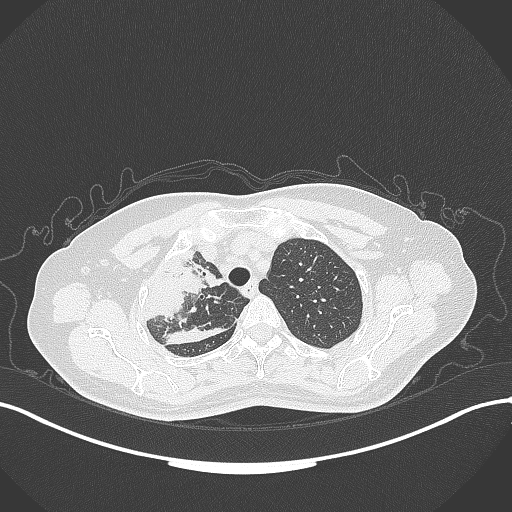
Chest CT, one axial slice; position 259 of 309 along the scan axis; reconstruction kernel B70f; lung window (W 1500 / L -600 HU); 512 × 512 image matrix, field of view 400 × 400 mm. Patient: female, 60 years. From the clinical record (not read from this slice): clinical TNM (as recorded): T3 N1 M1.
Outlined on this slice (rectangle marked by the reading radiologist):
- lung tumour (recorded histology: adenocarcinoma): bounding box (x1, y1, x2, y2) in pixels: (140, 254, 222, 335)